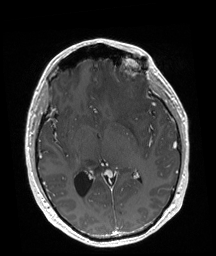
Brain MRI from a brain-tumour surgery series, one axial slice. Position 97 of 192 along the scan axis. T1-weighted post-contrast. 1 mm slice thickness. 216 × 256 image matrix, field of view 219 × 260 mm. Case-level facts recorded for this patient, not image findings: tumour location: Left Frontal.
Outlined on this slice (expert manual segmentation):
- tumour: box from (x=127, y=69) to (x=130, y=72) px